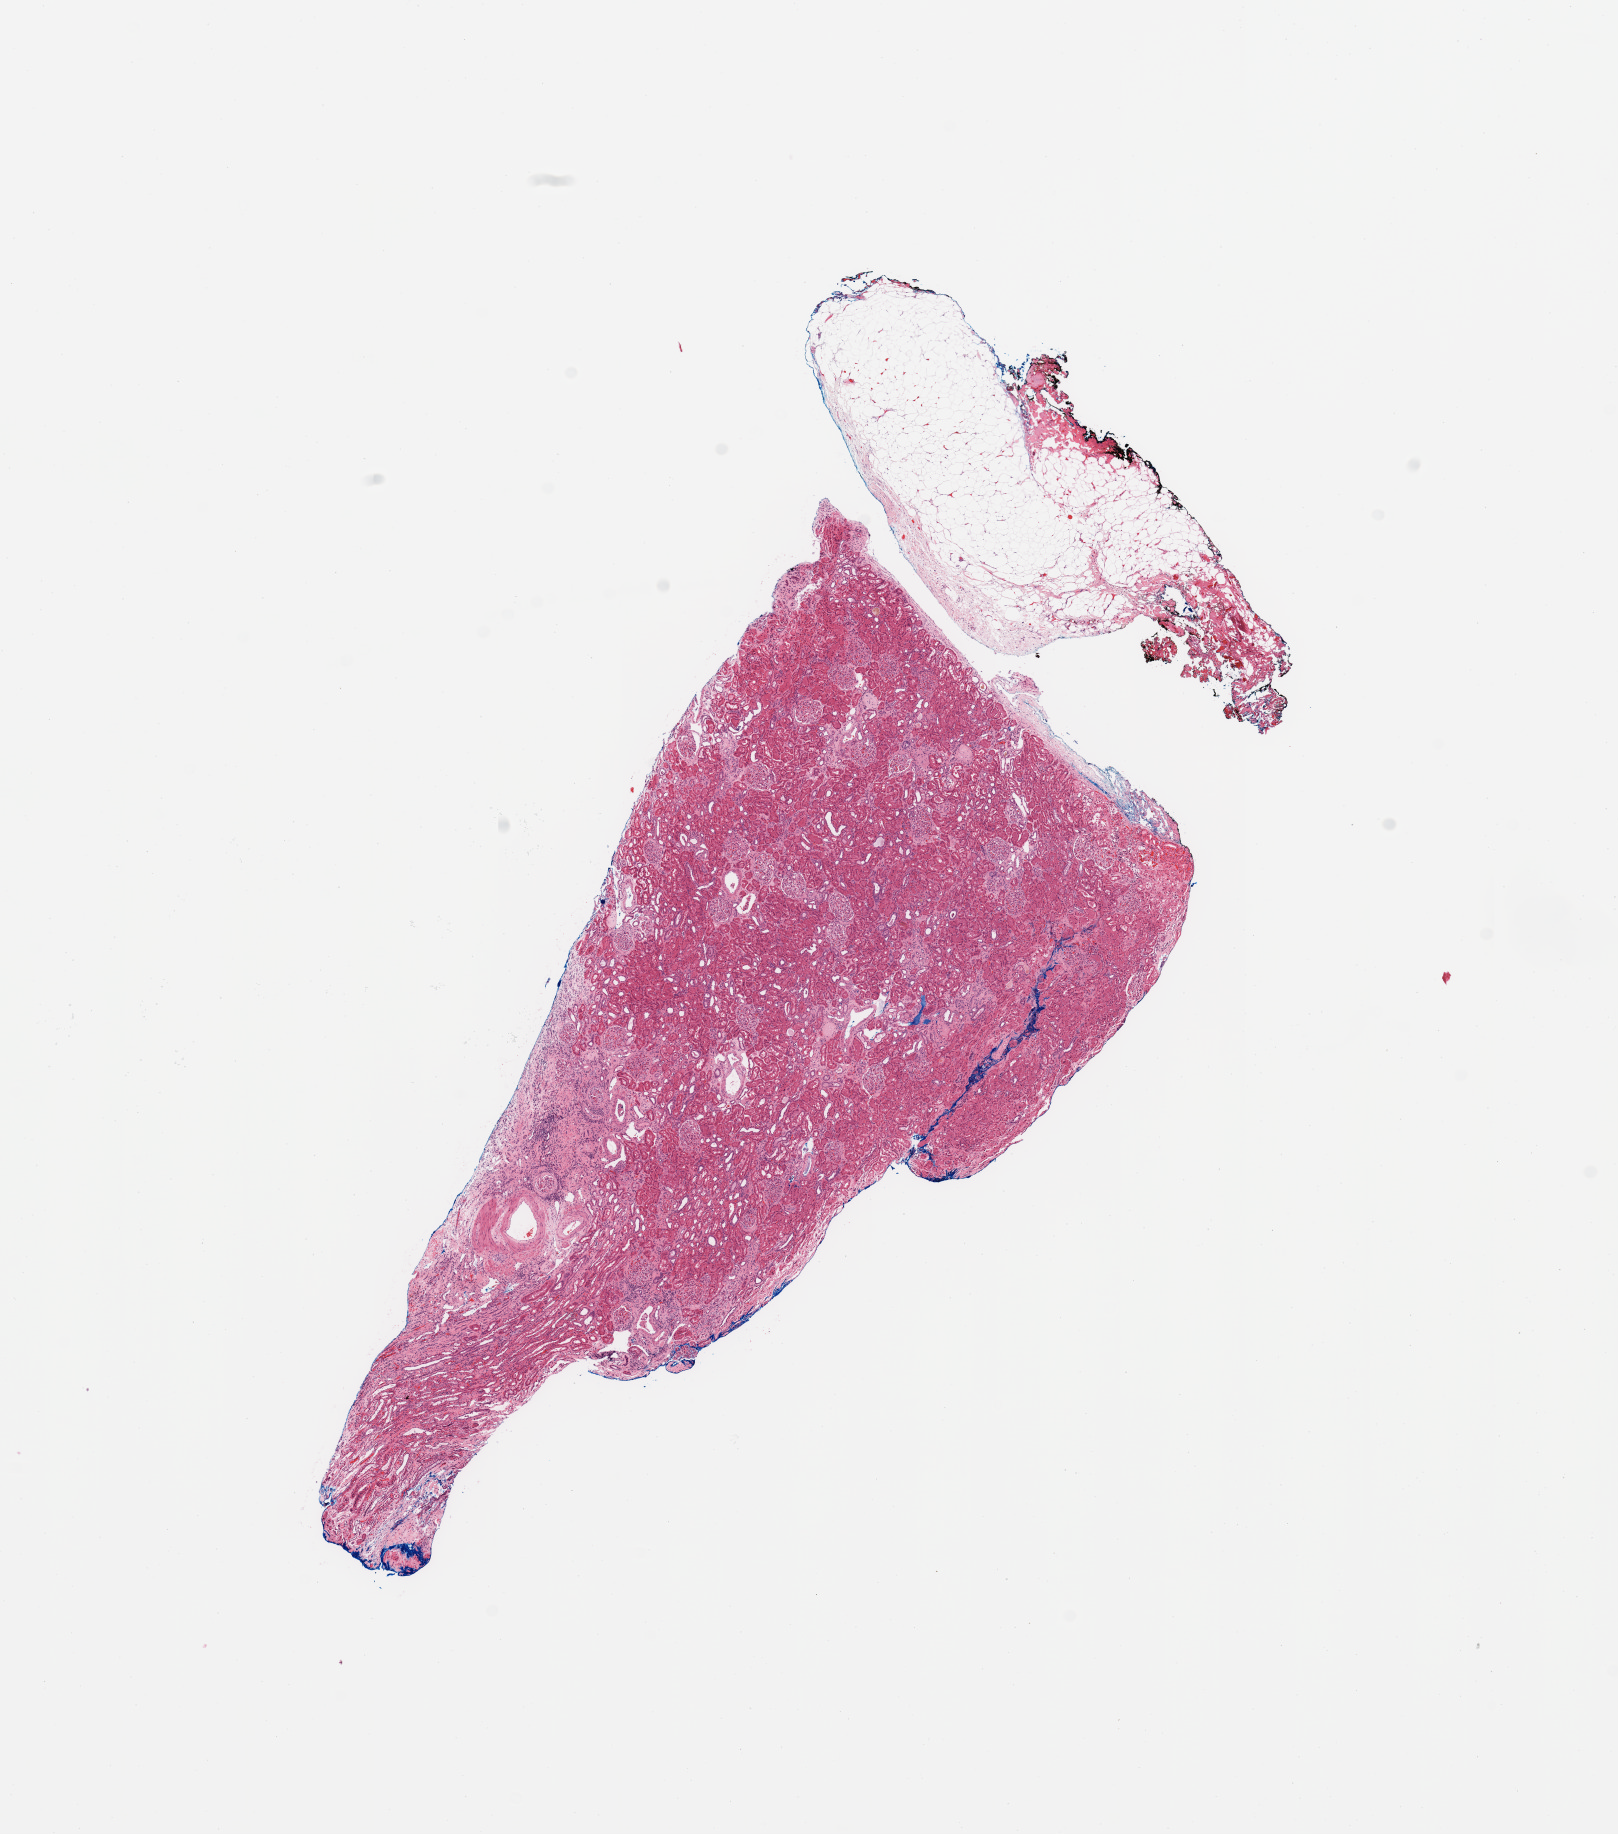
Hematoxylin and eosin (H&E) stained whole-slide image, a low-resolution overview of the entire scanned area, about 12.8 x 14.5 mm (slide scanned at 20x). Normal (non-tumour) tissue sample, sampled site: kidney. 56-year-old male patient.
* this section: normal (non-tumour) tissue from the same patient
* patient diagnosis: Renal cell carcinoma, NOS